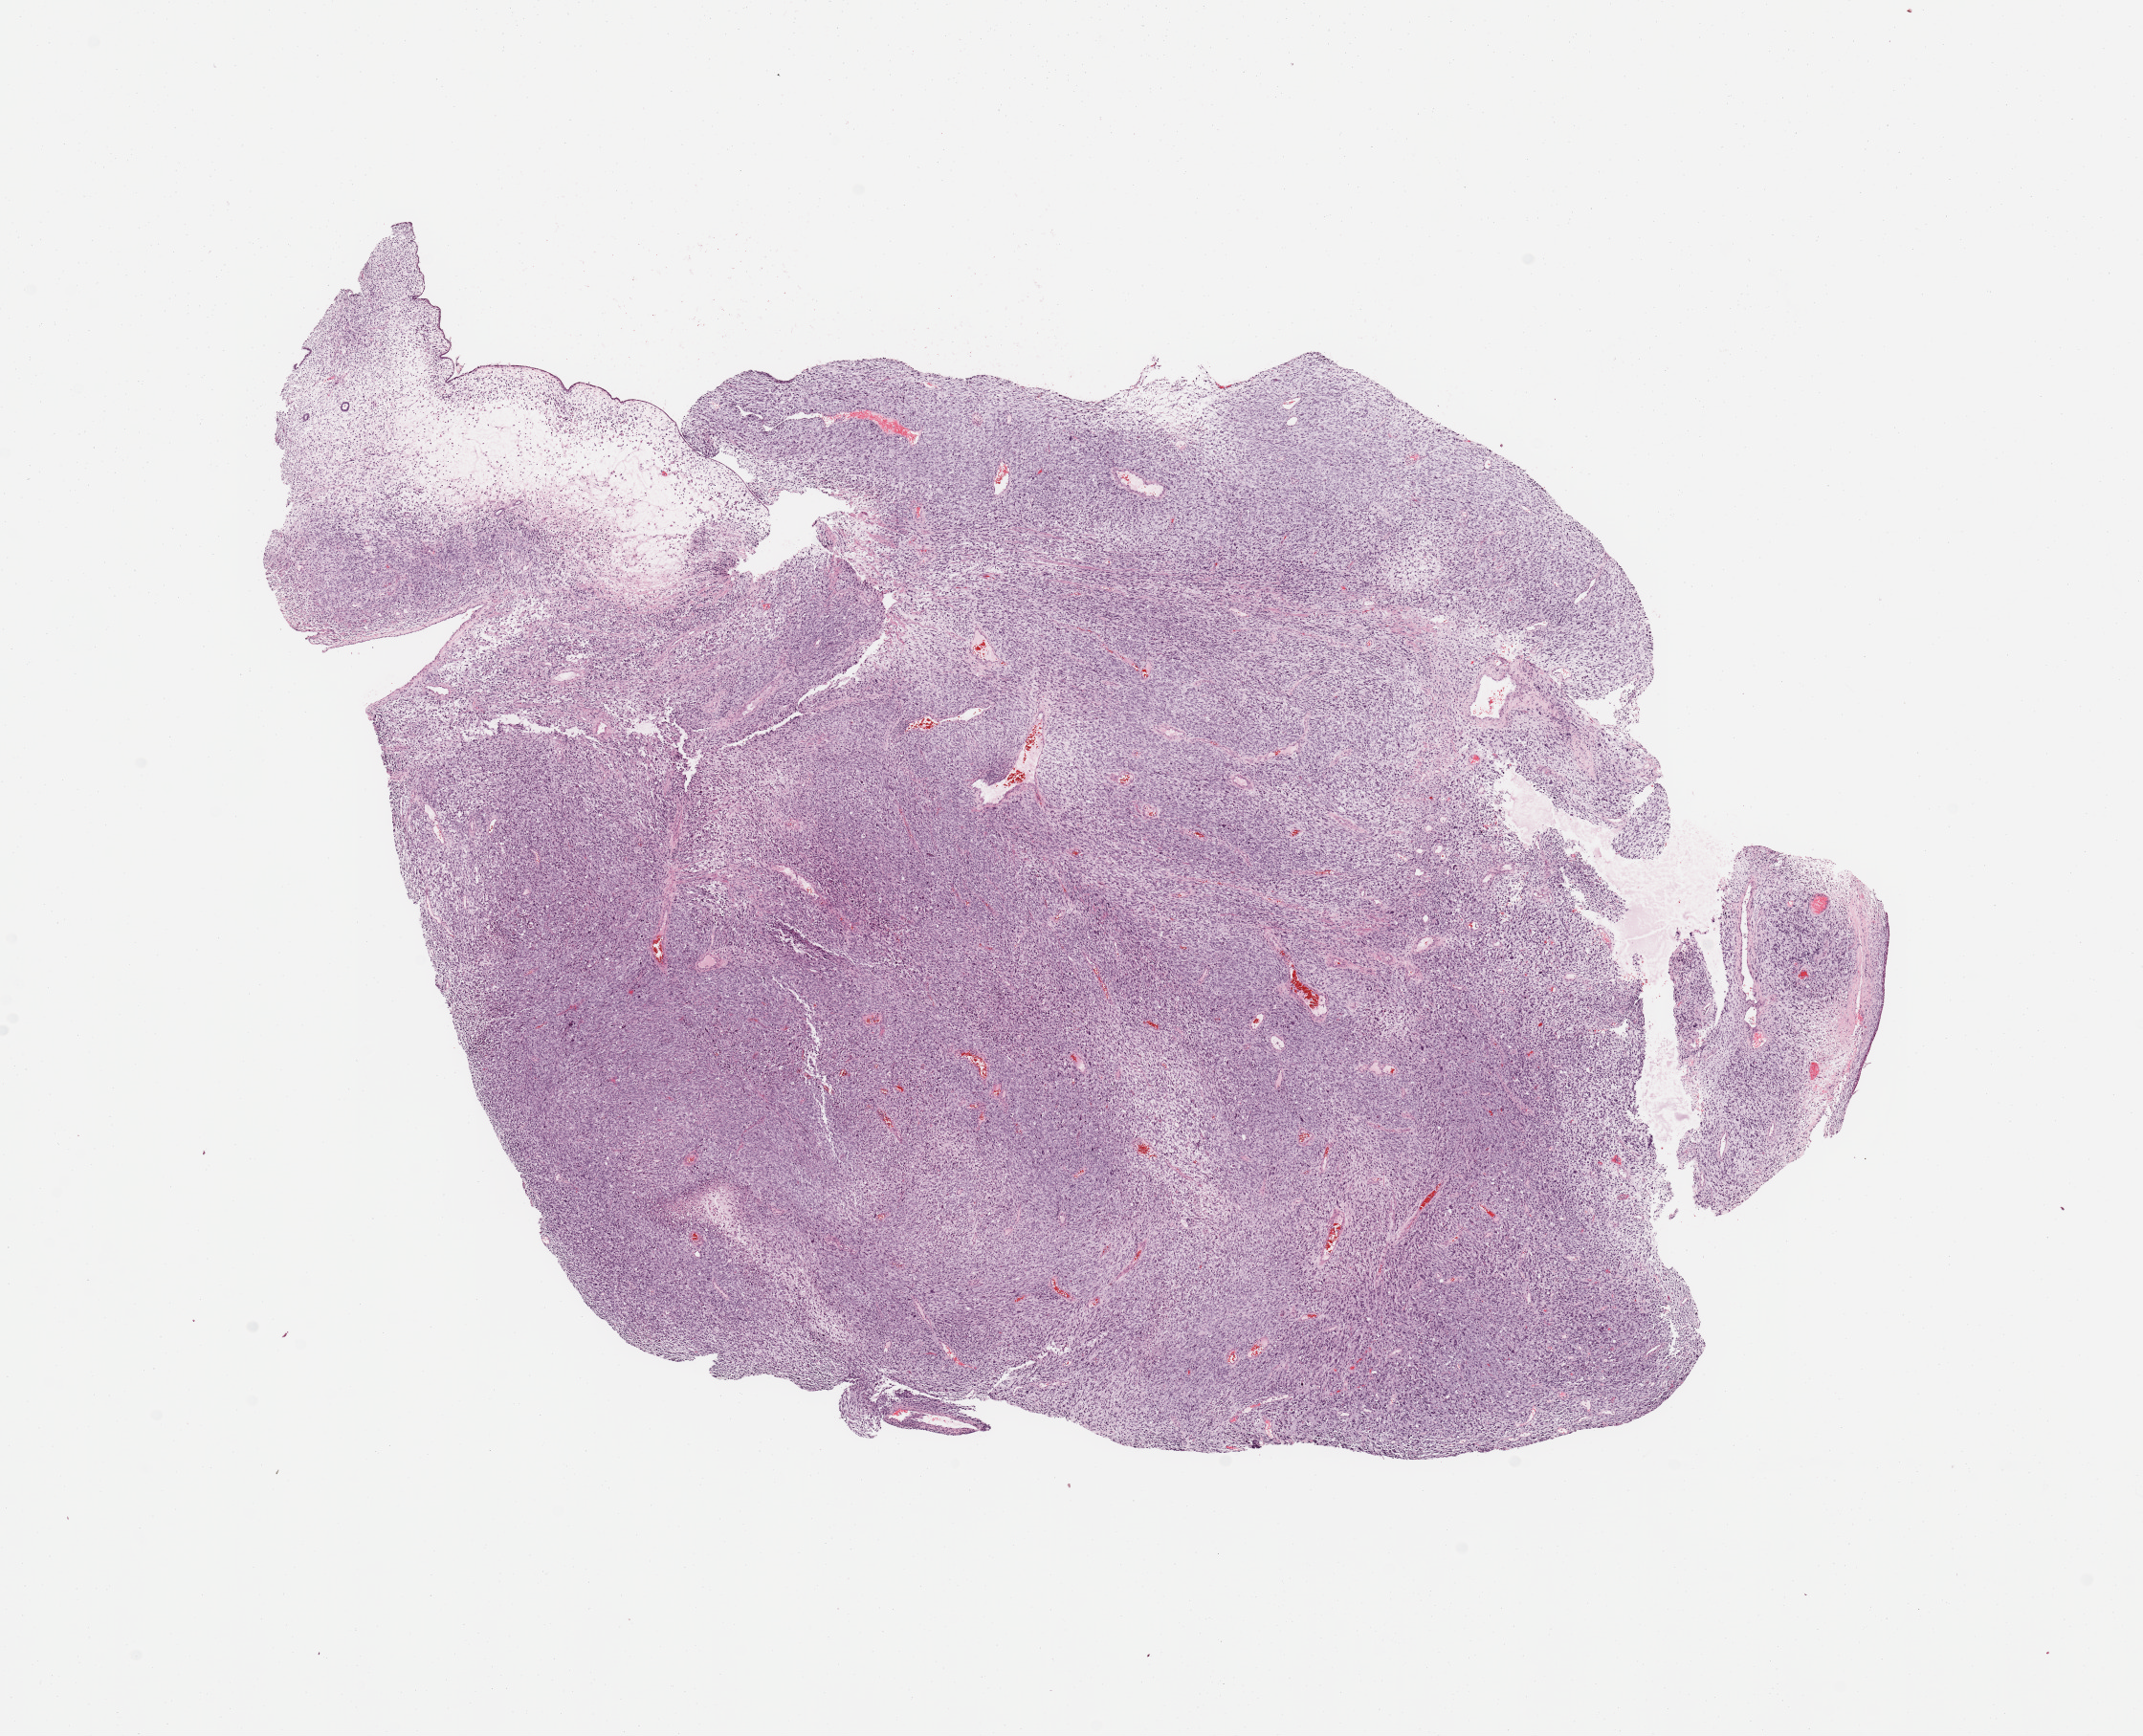
Digitized Hematoxylin and eosin (H&E) stained tissue section (whole slide), low-resolution overview of the scanned area, about 17.7 x 14.4 mm (from a 20x scan). Female, 62 y/o.
Patient diagnosis (cohort enrolment): sarcoma (site not recorded at cohort level).